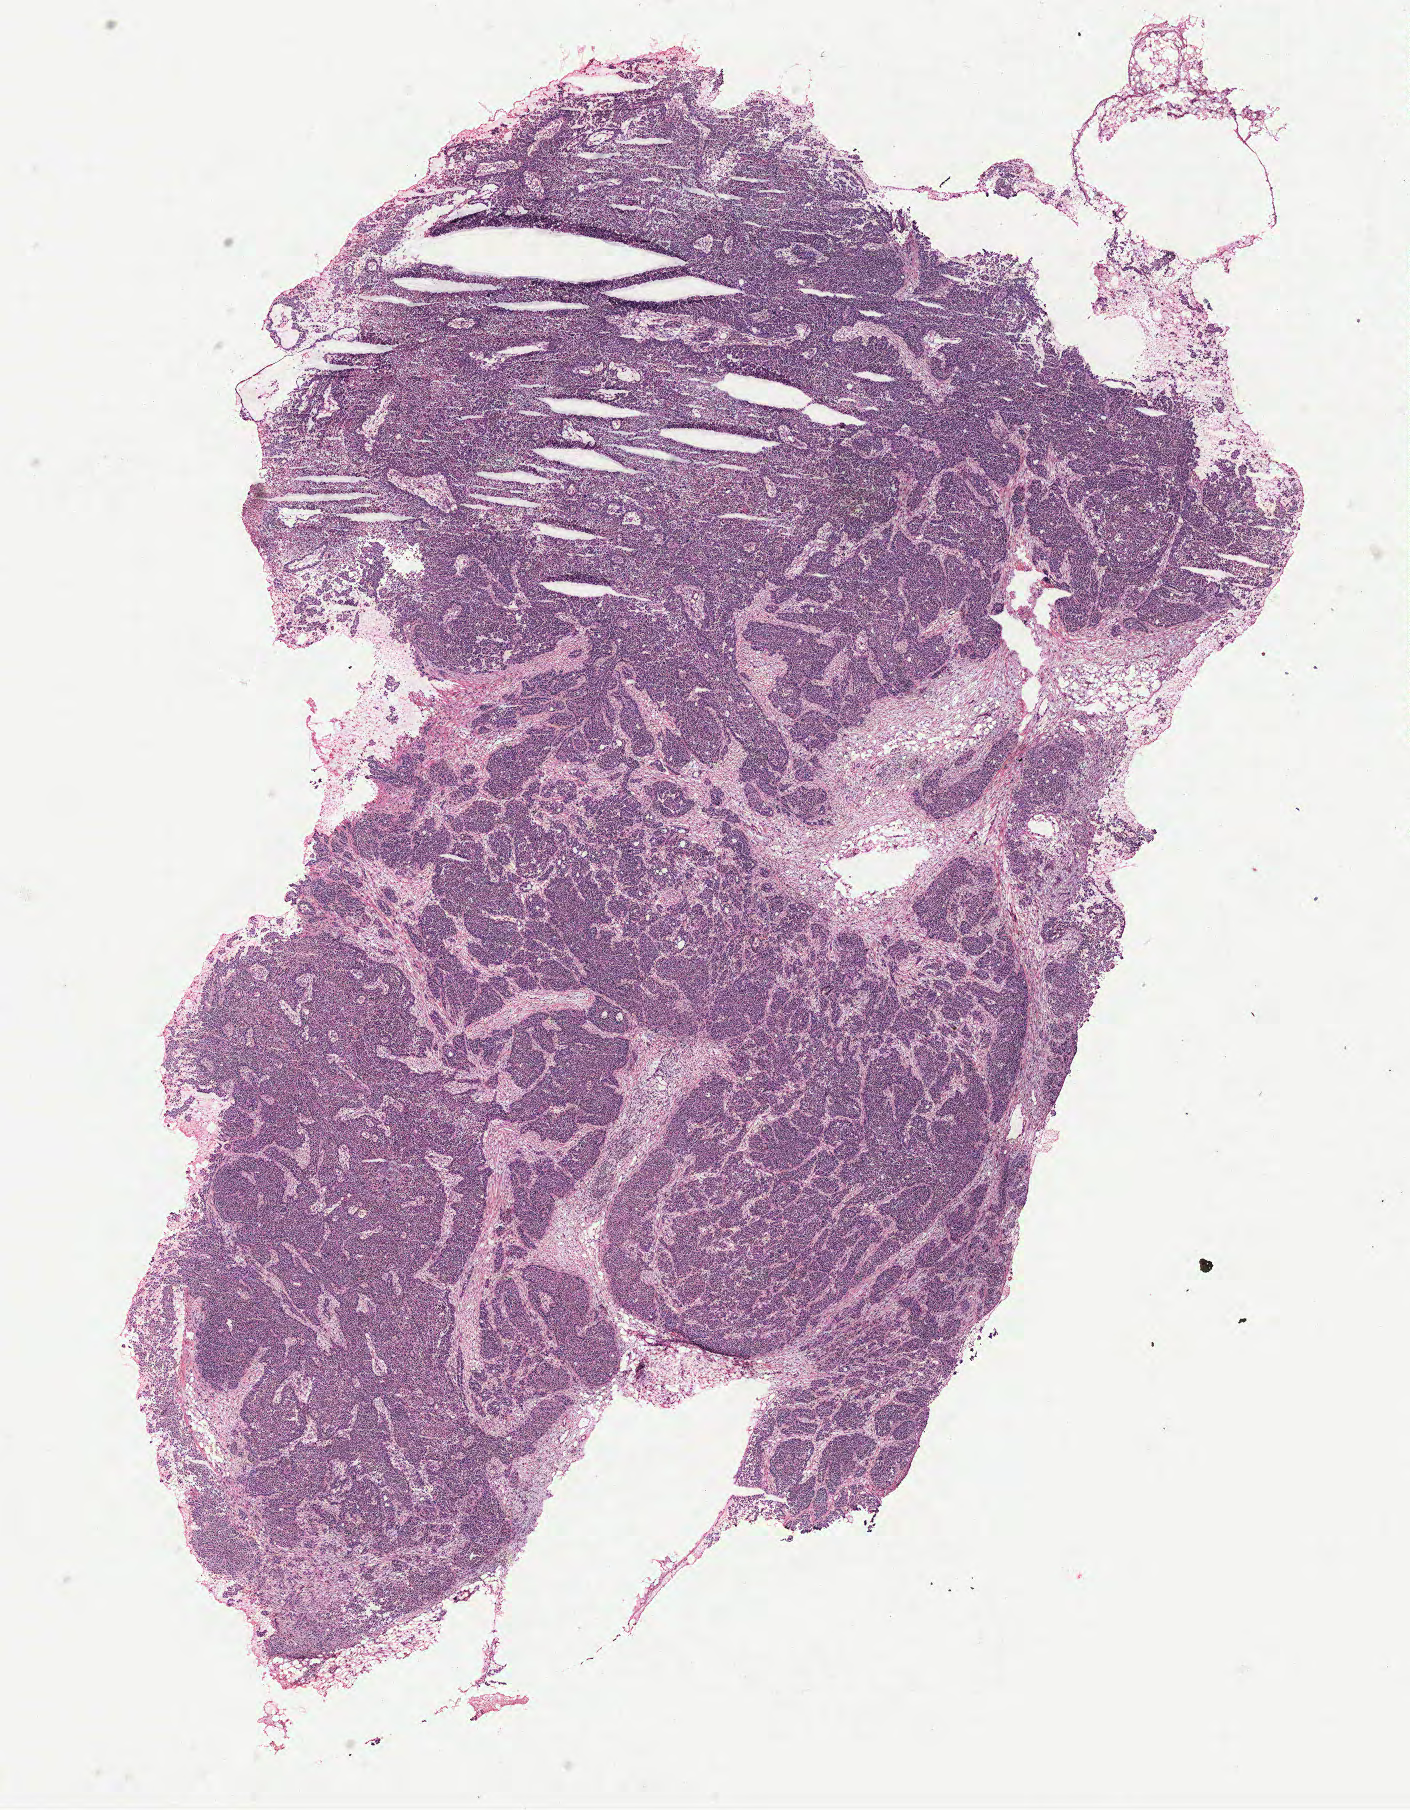
H&E-stained whole-slide image — shown as a low-resolution overview of the whole scanned area (about 11.3 x 14.5 mm, acquisition: 40x scan); ovary, tissue type not recorded.
Patient diagnosis (cohort enrolment): ovarian cancer (ovary).